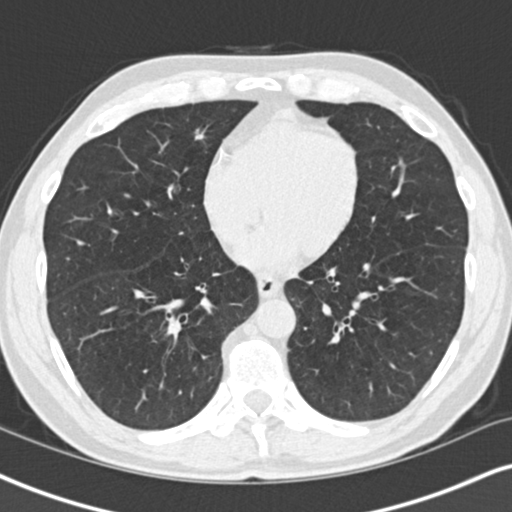
Low-dose screening chest CT, one axial slice; slice 45 of 148 in the series (ordered by position); reconstruction kernel B30f; lung window (W 1500 / L -600 HU); 2 mm slice thickness; 512 × 512 image matrix, field of view 328 × 328 mm.
Structures marked on this image (manually delineated by an expert):
- lesion 1 (tumor, middle lobe of right lung): bounding box <195,129,204,140> (left, top, right, bottom; pixels)